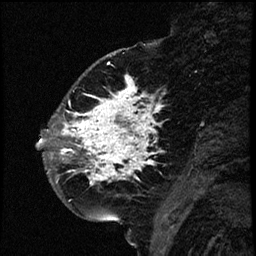
Breast MRI (dynamic contrast-enhanced), one sagittal slice. Slice 22 of 66 in the series (ordered by position). Dynamic contrast-enhanced study with each time point stored as its own series, time point 2 of 3 at this slice position (early post-contrast, ordered by acquisition time). 1.5 T. TE 4.2 ms, TR 17.6 ms. 256 × 256 image matrix. Female patient. From the clinical record (not read from this slice): setting: breast cancer imaged before/during neoadjuvant chemotherapy; receptor status: HER2-positive.
Structures marked on this image (semi-automatically segmented with operator editing):
- analysis volume of interest (the breast-tissue region the enhancement analysis was run in; not a lesion): bounding box (x1, y1, x2, y2) in pixels: (52, 69, 177, 209)
- tumour enhancement mask (voxels above the 100 % enhancement threshold inside the analysis volume of interest): (52, 76, 161, 184)